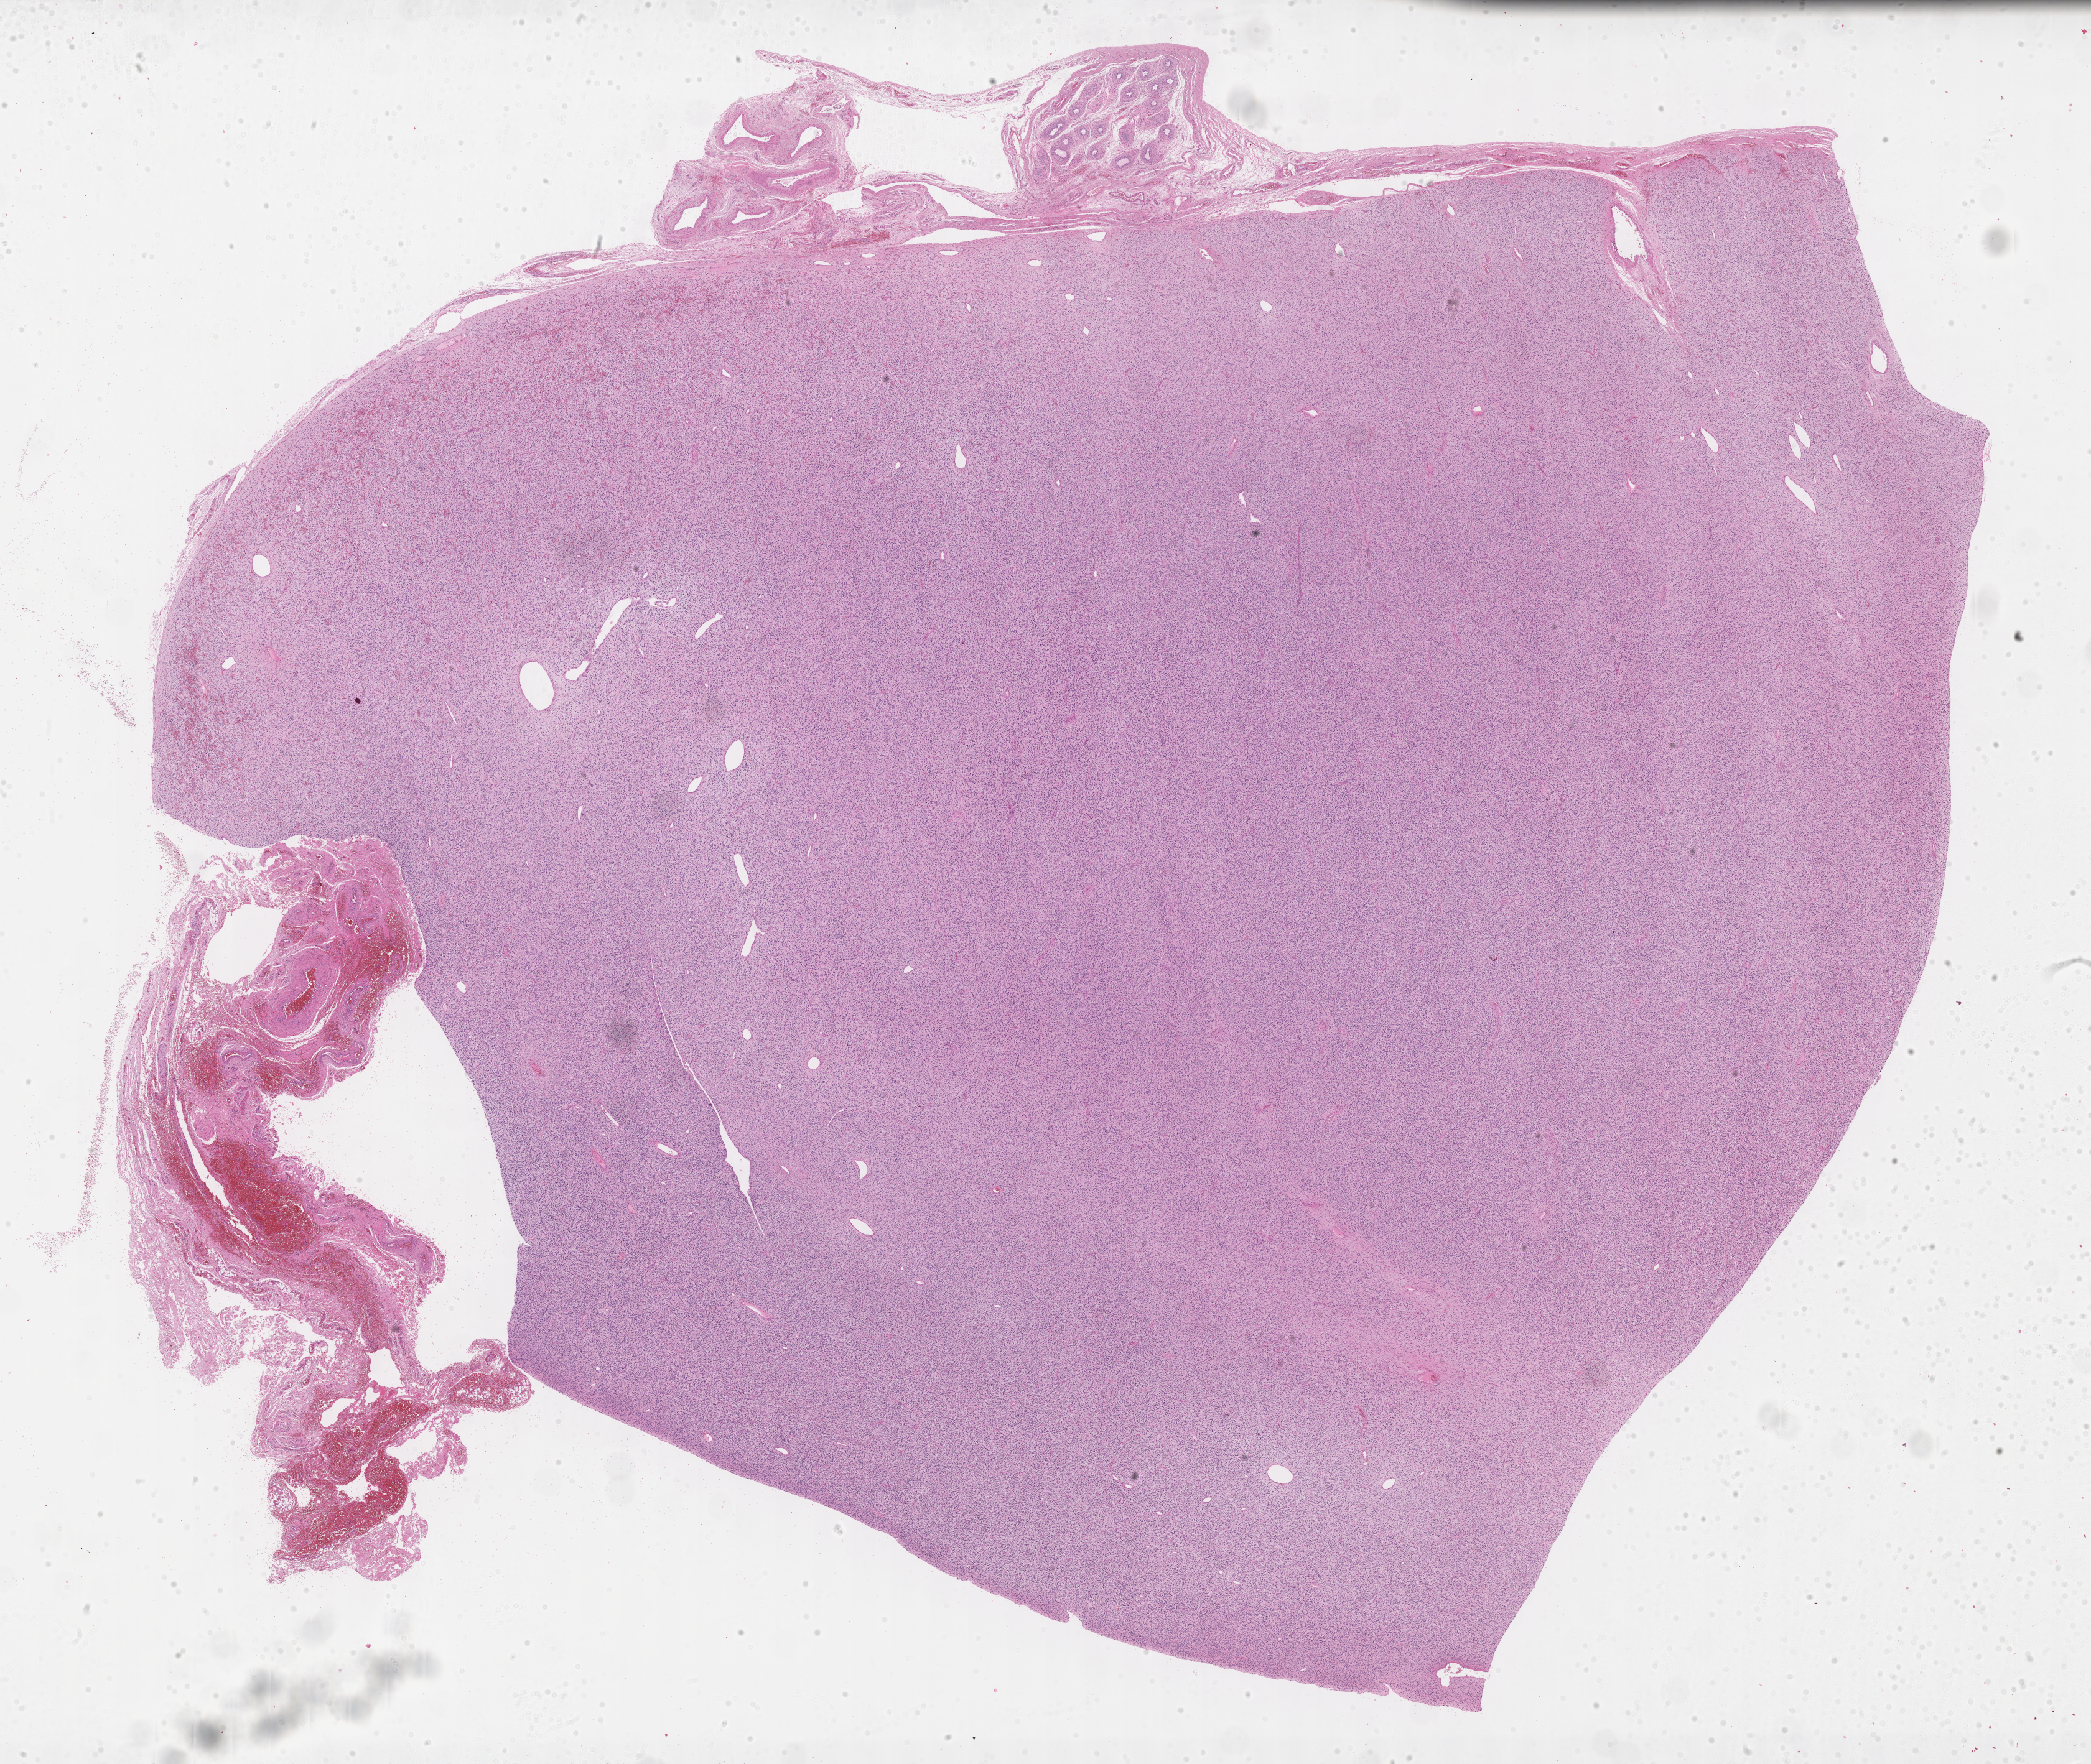
Digitized haematoxylin and eosin-stained section of tumor tissue — a low-resolution overview of the entire scanned area, about 27.2 x 22.9 mm. Formalin-fixed, paraffin-embedded (FFPE) tissue. Site: soft tissue - testicle, right. Male patient, age at diagnosis 9.3 years.
Diagnosis: rhabdomyosarcoma; histological classification: embryonal rhabdomyosarcoma.